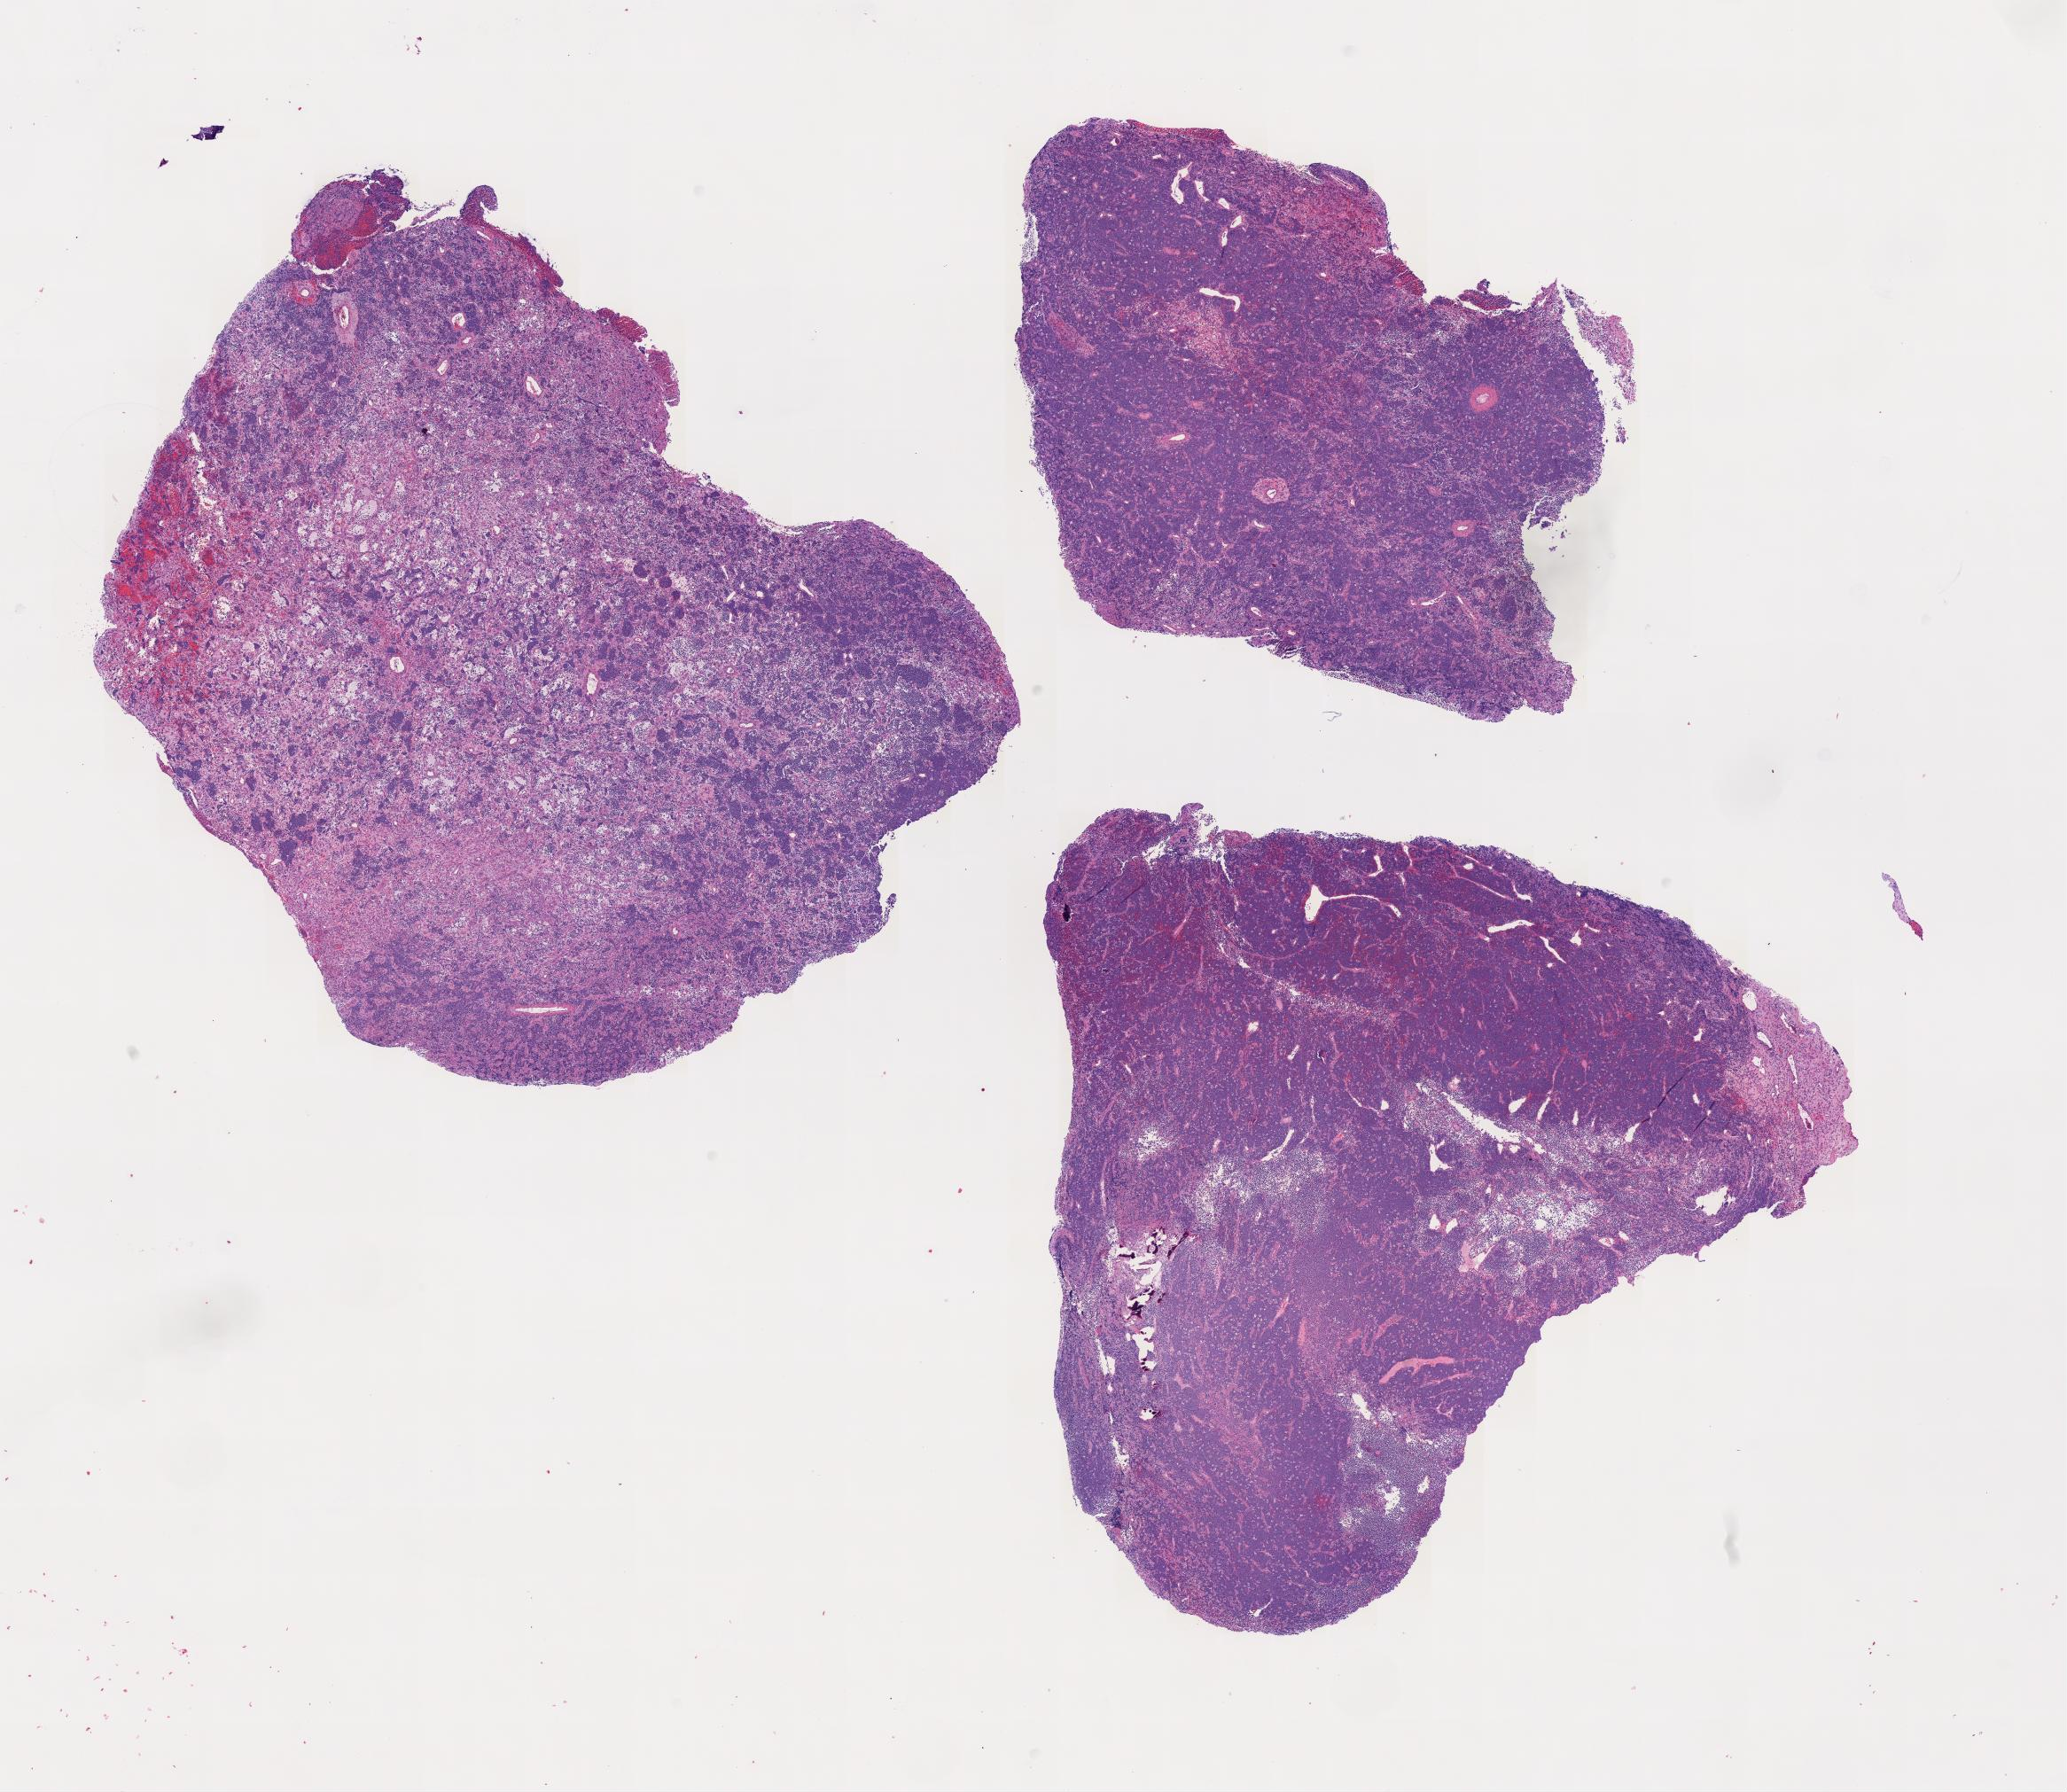
Whole-slide image, H&E stain, whole scanned area shown as a low-resolution overview. Specimen: tumor tissue. Anatomic site: cranium. Male, age 5 years at initial diagnosis.
Diagnosis: Burkitt lymphoma, NOS.